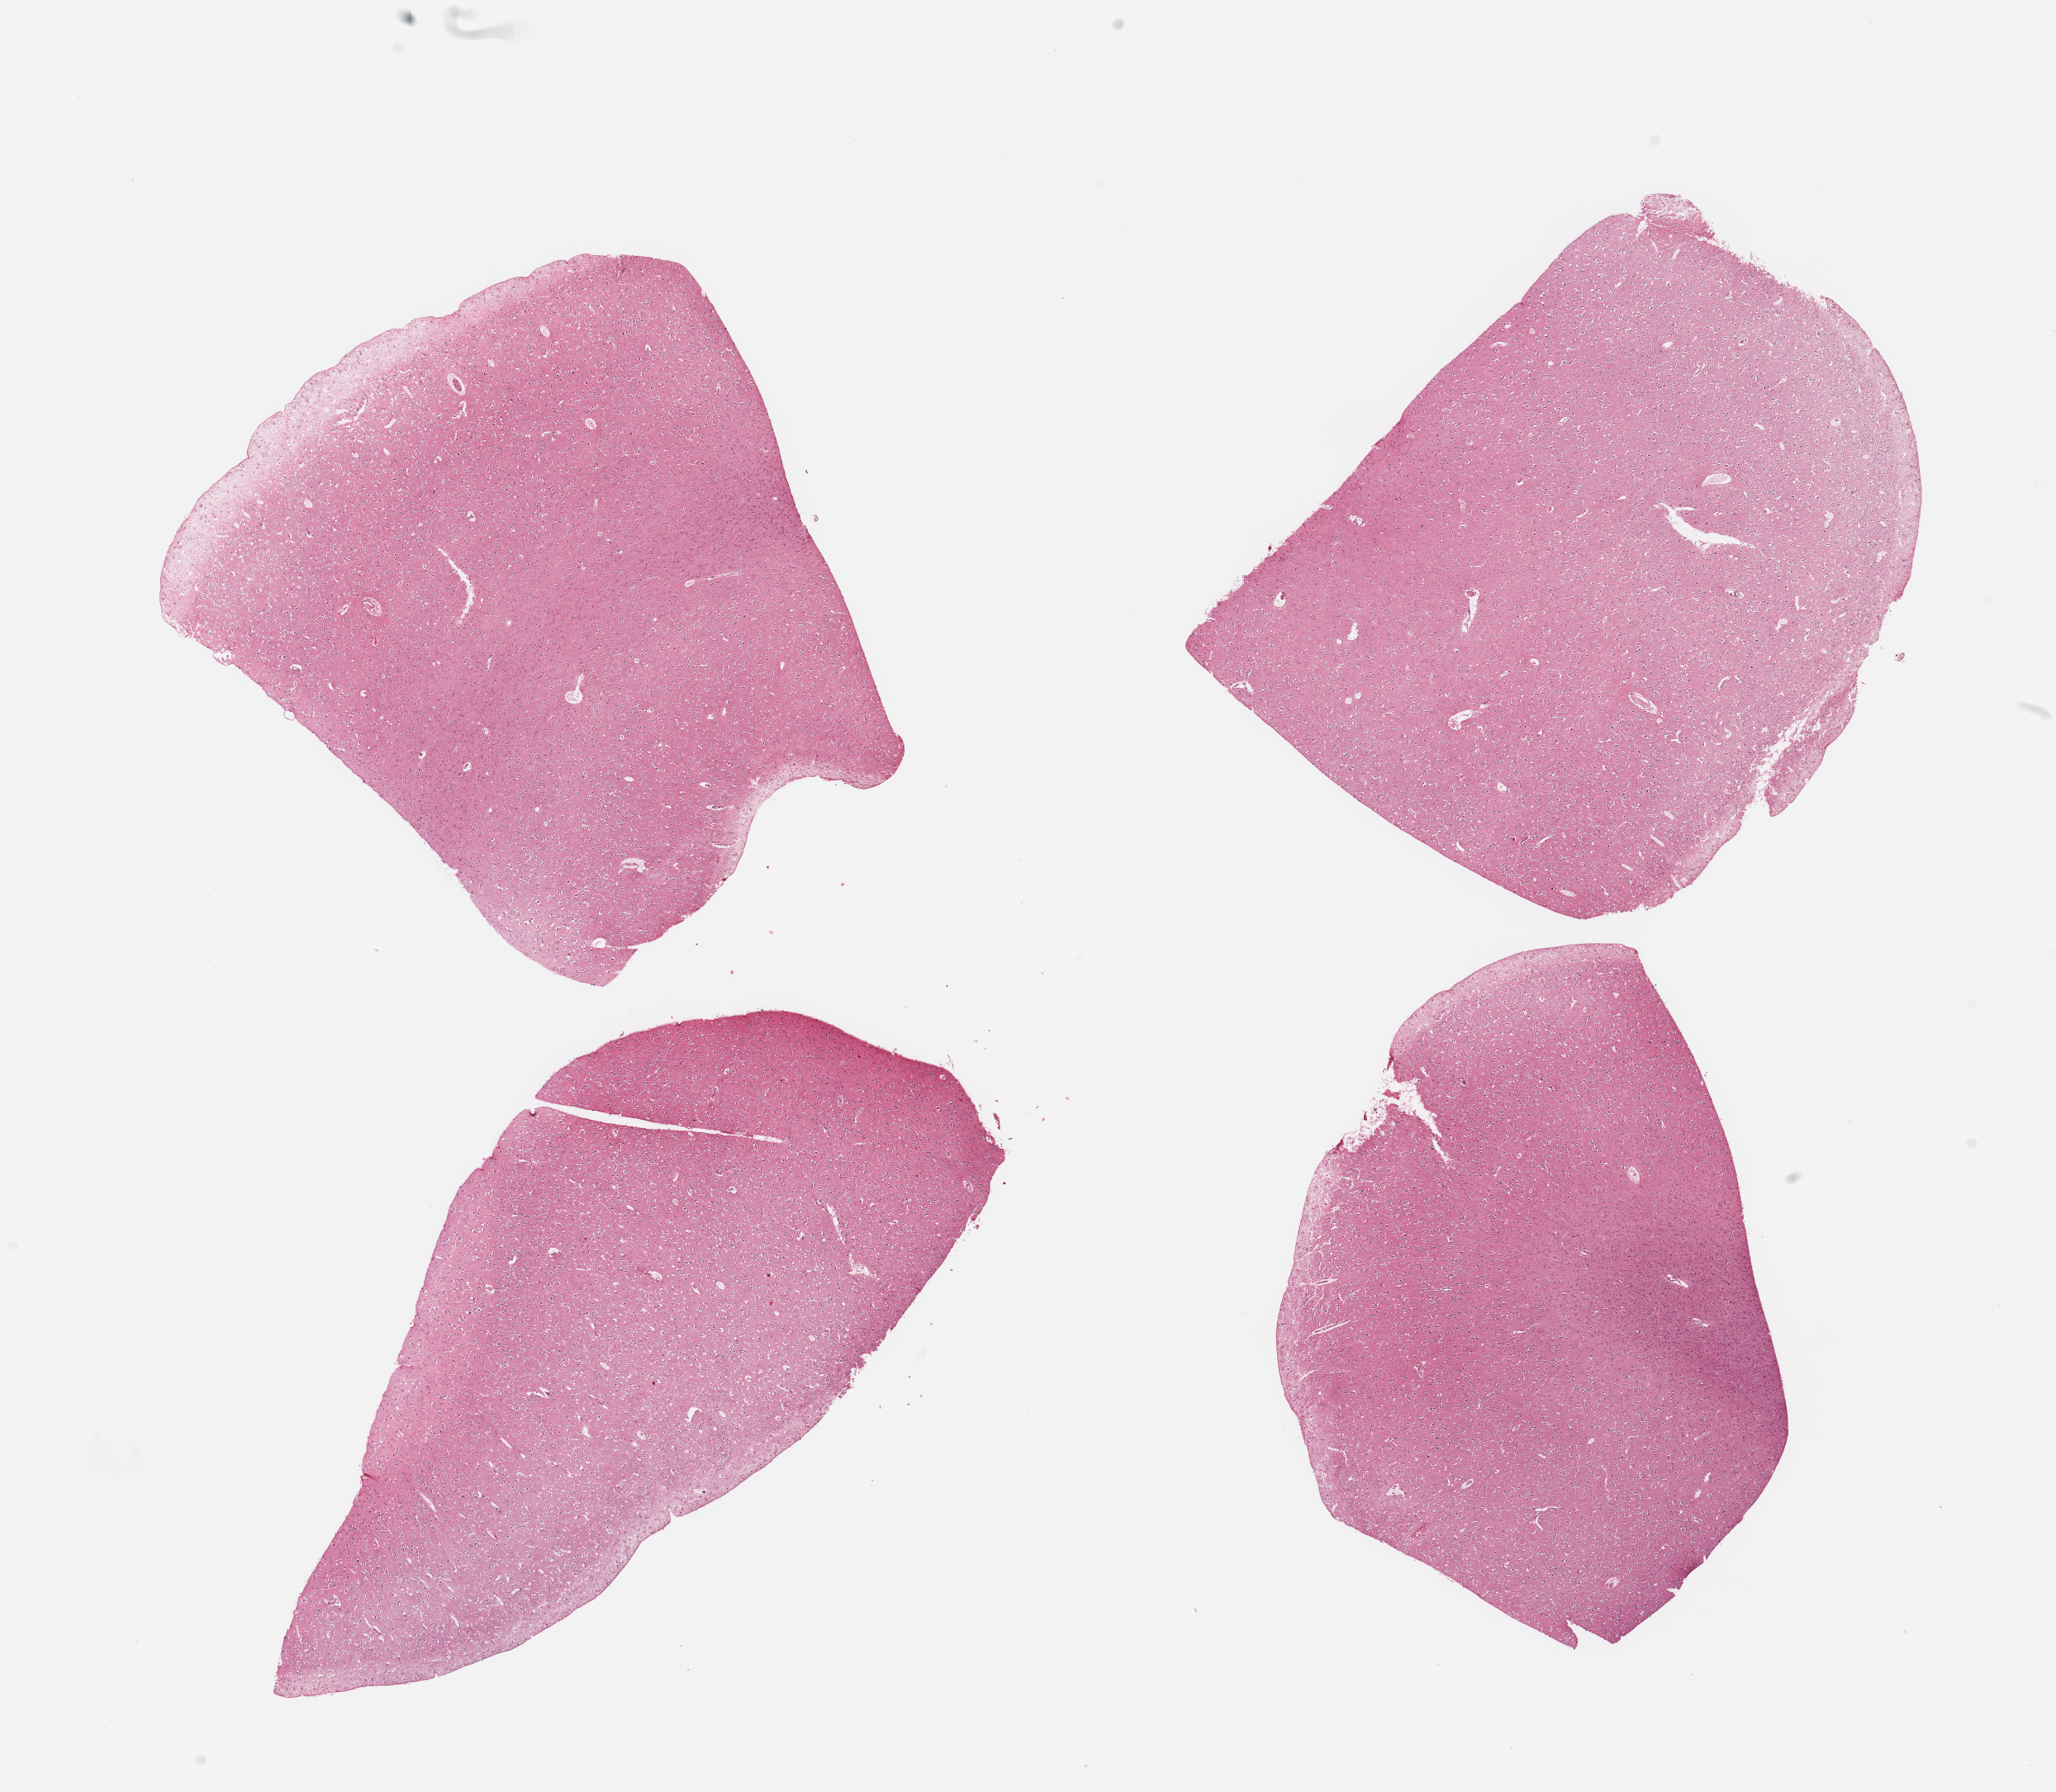
Haematoxylin and eosin whole-slide image, brightfield, whole scanned area (about 19.7 x 17.2 mm, acquisition: 20x scan) shown as a low-resolution overview, PAXgene-fixed paraffin-embedded (PFPE) section, sampled site (target tissue): cerebral cortex, donor tissue sample. Male donor.
Reviewer comment on this tissue sample: 4 pieces.